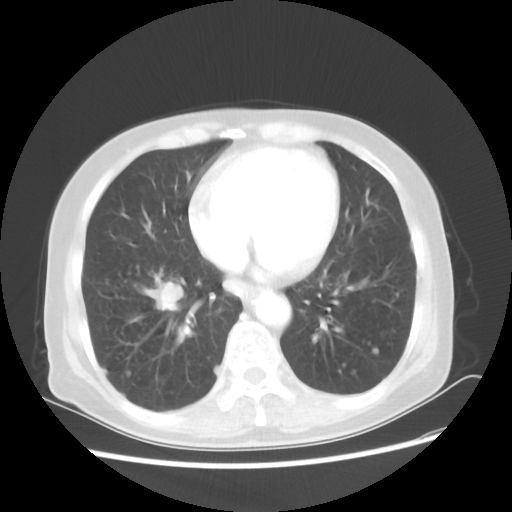
Chest CT, one axial slice. Slice 20 of 56 in the series (ordered by position). 80 kVp. Lung window (W 1500 / L -600 HU). 512 × 512 image matrix, field of view 360 × 360 mm. Female patient, age 68 years. Case-level facts recorded for this patient, not image findings: clinical TNM (as recorded): T1c N3 M0.
Annotated regions visible in this slice (bounding box drawn by a radiologist):
- lung tumour (recorded histology: squamous cell carcinoma): box from (x=137, y=265) to (x=197, y=318) px